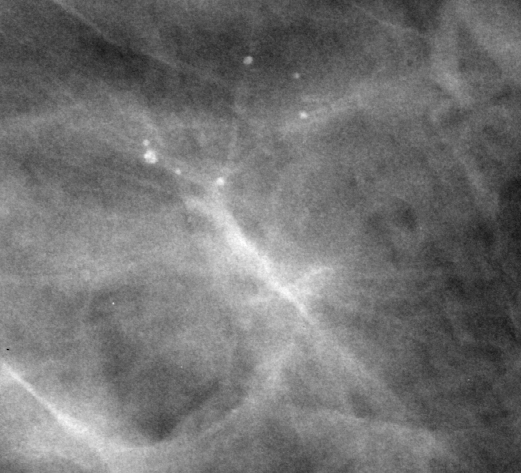
Crop from a digitized film mammogram around one marked abnormality, right breast, CC view, BI-RADS breast density category 3 (scale 1–4).
Calcifications, morphology round and regular, distribution clustered; BI-RADS assessment category 4; subtlety rating 4 on a 1 (subtle) to 5 (obvious) scale; pathology (as recorded): benign.